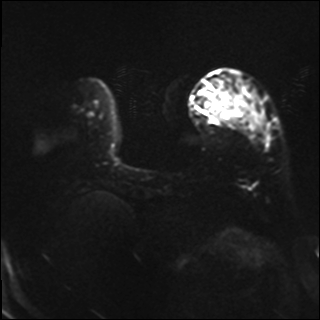
Breast MRI, one axial slice. Slice 8 of 37 in the series (ordered by position). Diffusion-weighted series; image 2 of 4 stored at this slice position (different b-values; order by instance number). 1.5 T. 4 mm slice thickness. 320 × 320 image matrix, field of view 320 × 320 mm. Female patient.
Structures marked on this image (expert manual segmentation):
- tumour on diffusion-weighted imaging: bounding box <223,95,245,121> (left, top, right, bottom; pixels)